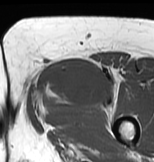
MRI of an extremity soft-tissue mass, one axial slice. Position 38 of 83 along the scan axis. MR volume resampled by the dataset authors to the PET/CT grid (not the native acquisition matrix). 3.27 mm slice thickness. 154 × 162 image matrix. Female patient. Case-level facts recorded for this patient, not image findings: histological type: myxofibrosarcoma; grade: intermediate; site of the primary tumour: left thigh.
Structures marked on this image (expert contour drawn on MRI and transferred to this co-registered scan by the dataset authors):
- gross tumour volume including surrounding oedema: box from (x=28, y=57) to (x=120, y=122) px
- gross tumour volume (mass): (x=35, y=57)–(x=109, y=108)